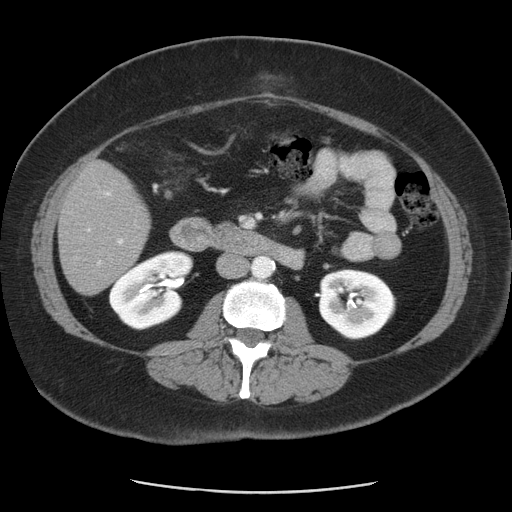
Contrast-enhanced abdominal CT, one axial slice. Position 14 of 55 along the scan axis. Reconstruction kernel STANDARD. Intravenous contrast given. Soft-tissue window (W 400 / L 40 HU). 5 mm slice thickness. 512 × 512 image matrix, field of view 380 × 380 mm. Female patient, age 52 years. From the clinical record (not read from this slice): diagnosis: colorectal cancer liver metastases, imaged before liver resection; multiple liver metastases: yes; largest metastasis: 2.5 cm; disease in both lobes: yes.
Structures marked on this image (expert manual segmentation):
- liver: bounding box [x1, y1, x2, y2] px = [59, 161, 150, 296]
- planned liver remnant (the part of the liver to remain after resection): [59, 192, 138, 296]
- portal vein (with intrahepatic branches): [86, 189, 137, 278]